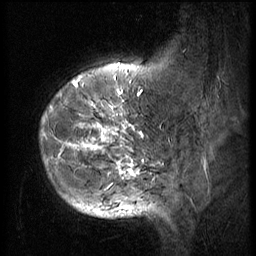
Breast MRI (dynamic contrast-enhanced), one sagittal slice; slice 13 of 56 in the series (ordered by position); 3 images stored at this slice position (order not interpretable as contrast timing); 1.5 T; TE 4.2 ms, TR 9 ms; 2.5 mm slice thickness; 256 × 256 image matrix, field of view 180 × 180 mm. Patient: female, 49 years. Case-level facts recorded for this patient, not image findings: setting: breast cancer imaged before/during neoadjuvant chemotherapy; receptor status: HER2-positive.
Annotated regions visible in this slice (semi-automatically segmented with operator editing):
- analysis volume of interest (the breast-tissue region the enhancement analysis was run in; not a lesion): bounding box [x1, y1, x2, y2] px = [33, 79, 152, 203]
- tumour enhancement mask (voxels above the 140 % enhancement threshold inside the analysis volume of interest): [43, 79, 144, 203]